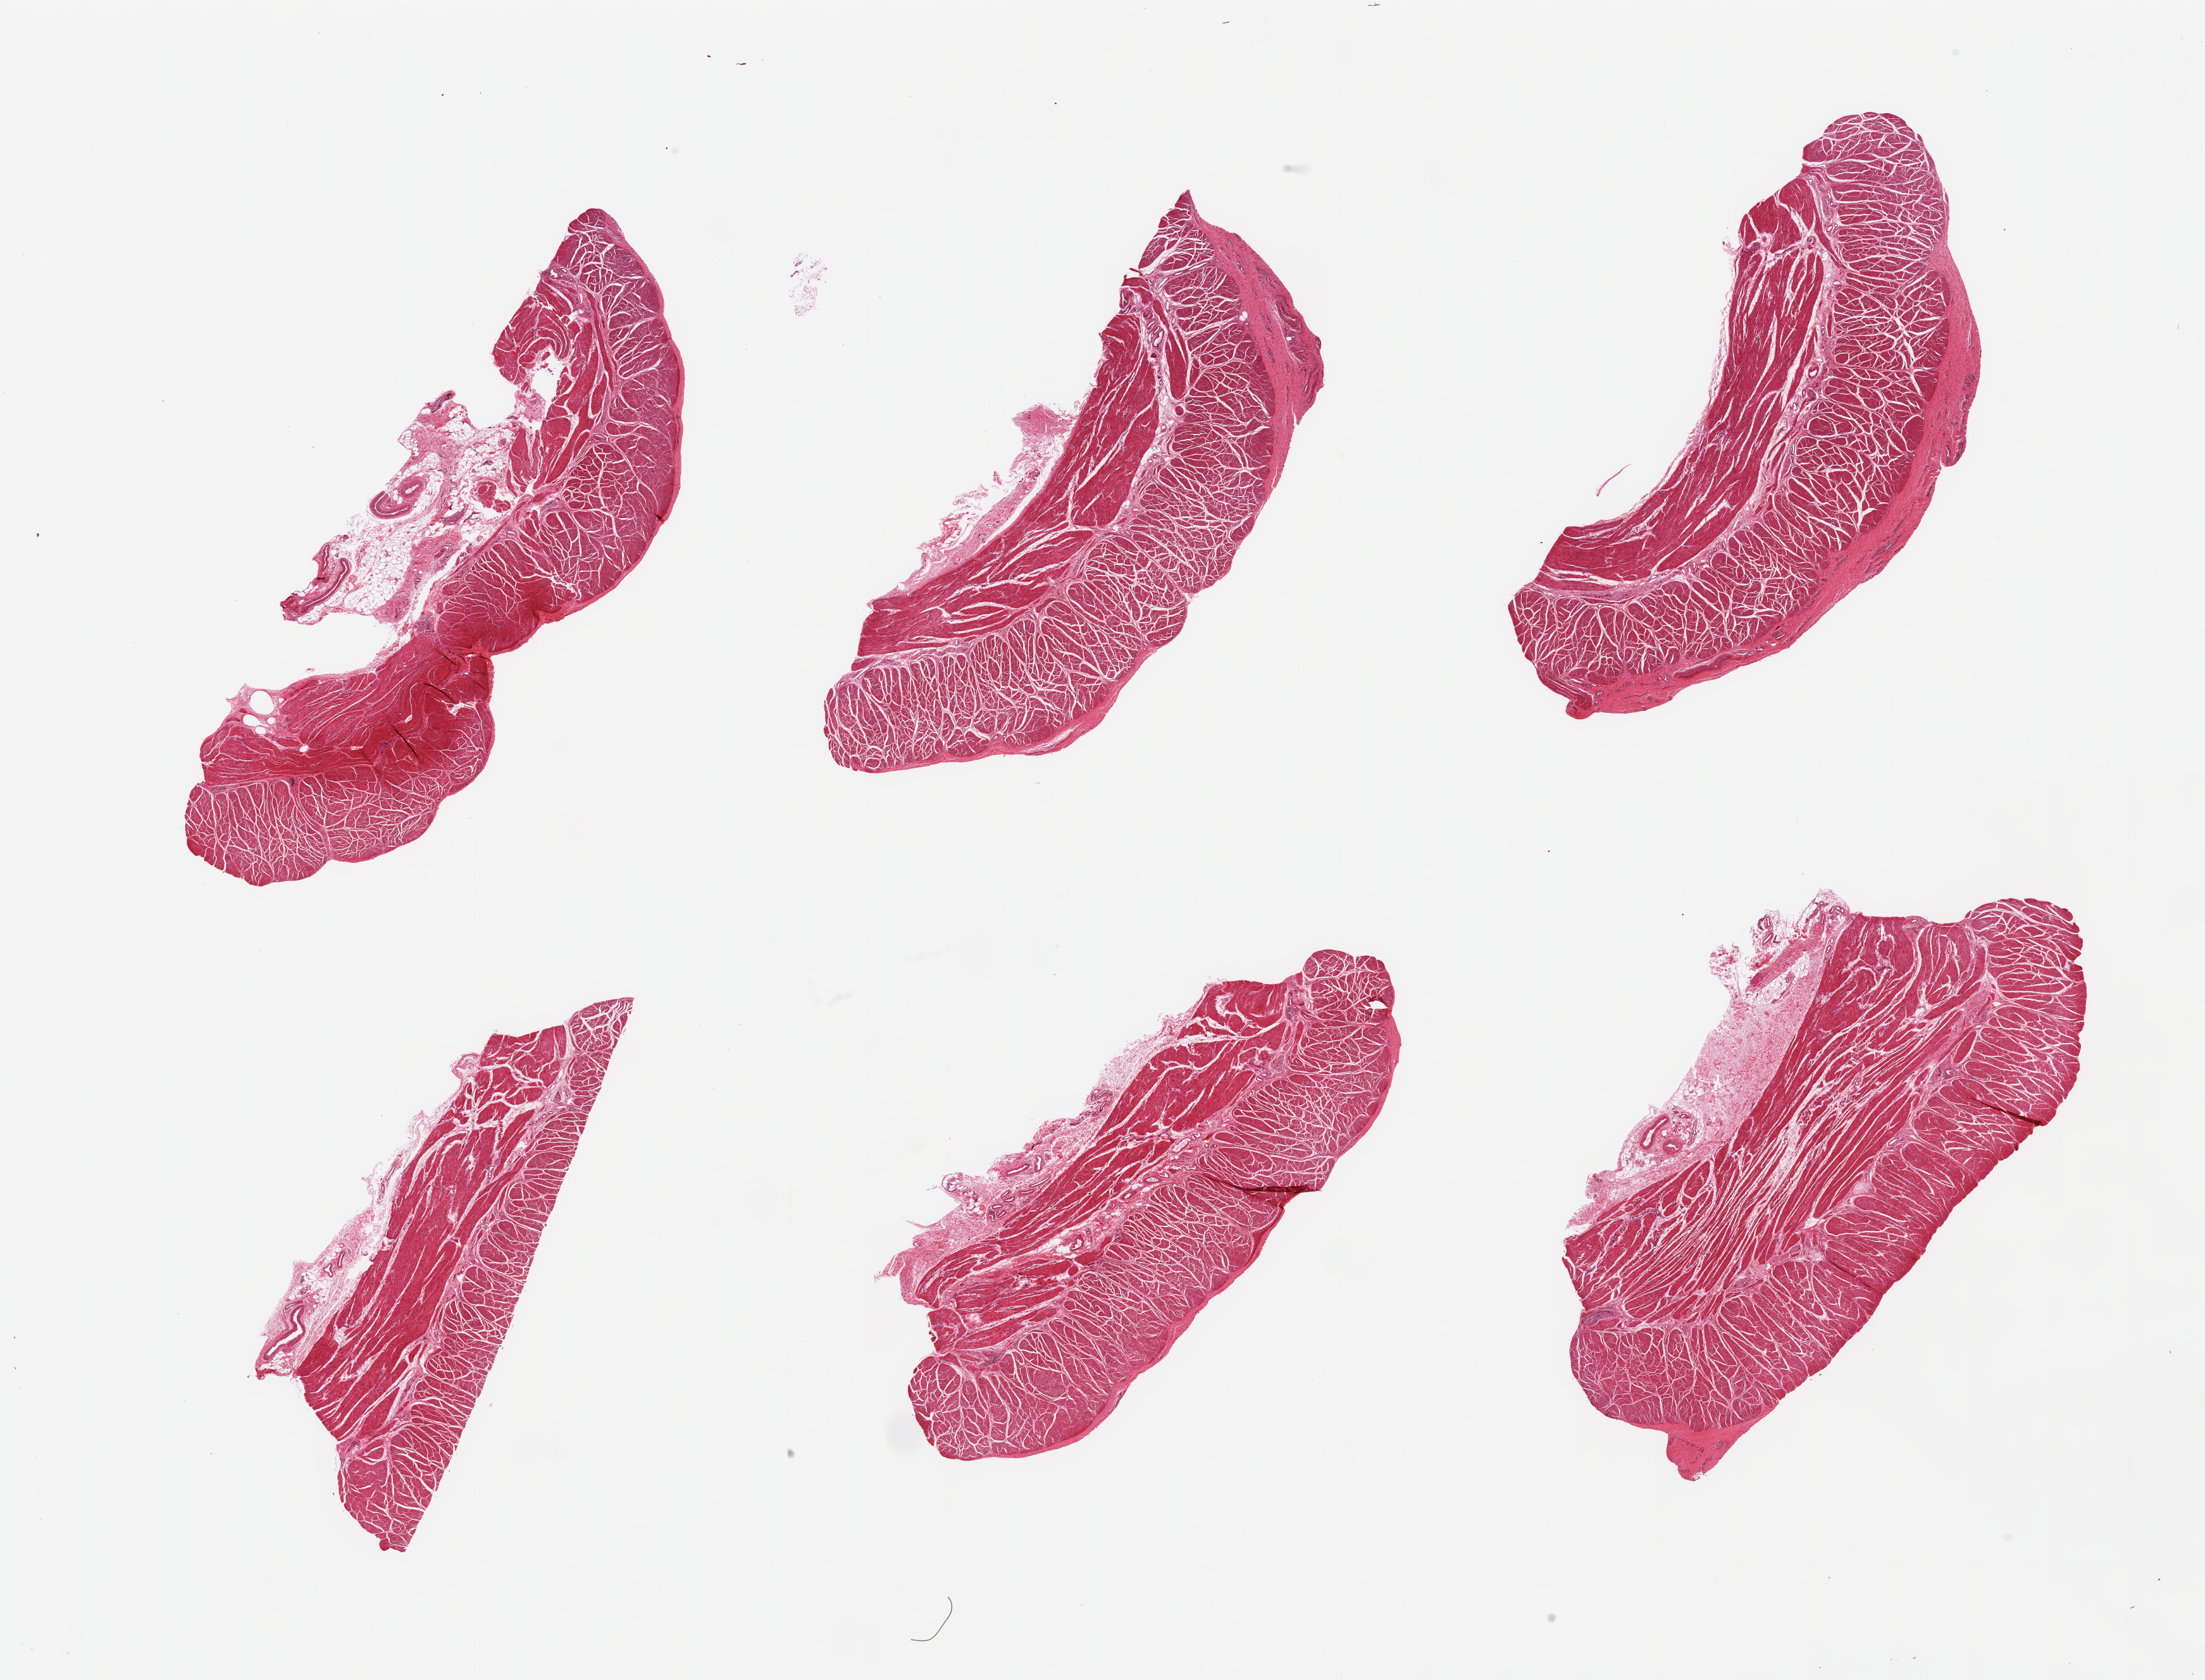
Whole-slide image, hematoxylin and eosin (H&E) stain — shown as a low-resolution overview of the whole scanned area (about 27.6 x 21.0 mm). PAXgene-fixed, paraffin-embedded tissue. Section of esophageal muscle (target tissue). Tissue donor sample. Donor sex: male.
Reviewer comment on this tissue sample: 6 pieces, confirmed target muscularis.